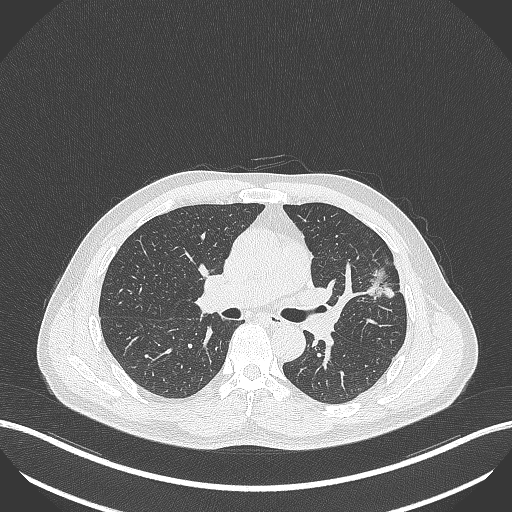
Chest CT, one axial slice; lung window (W 1500 / L -600 HU); 512 × 512 image matrix, field of view 400 × 400 mm. Patient: male, 55 years. From the clinical record (not read from this slice): clinical TNM (as recorded): T1c N0 M0; histopathological grade: G2-3.
Annotated regions visible in this slice (bounding box drawn by a radiologist):
- lung tumour (recorded histology: adenocarcinoma): bounding box [x1, y1, x2, y2] px = [362, 265, 397, 297]